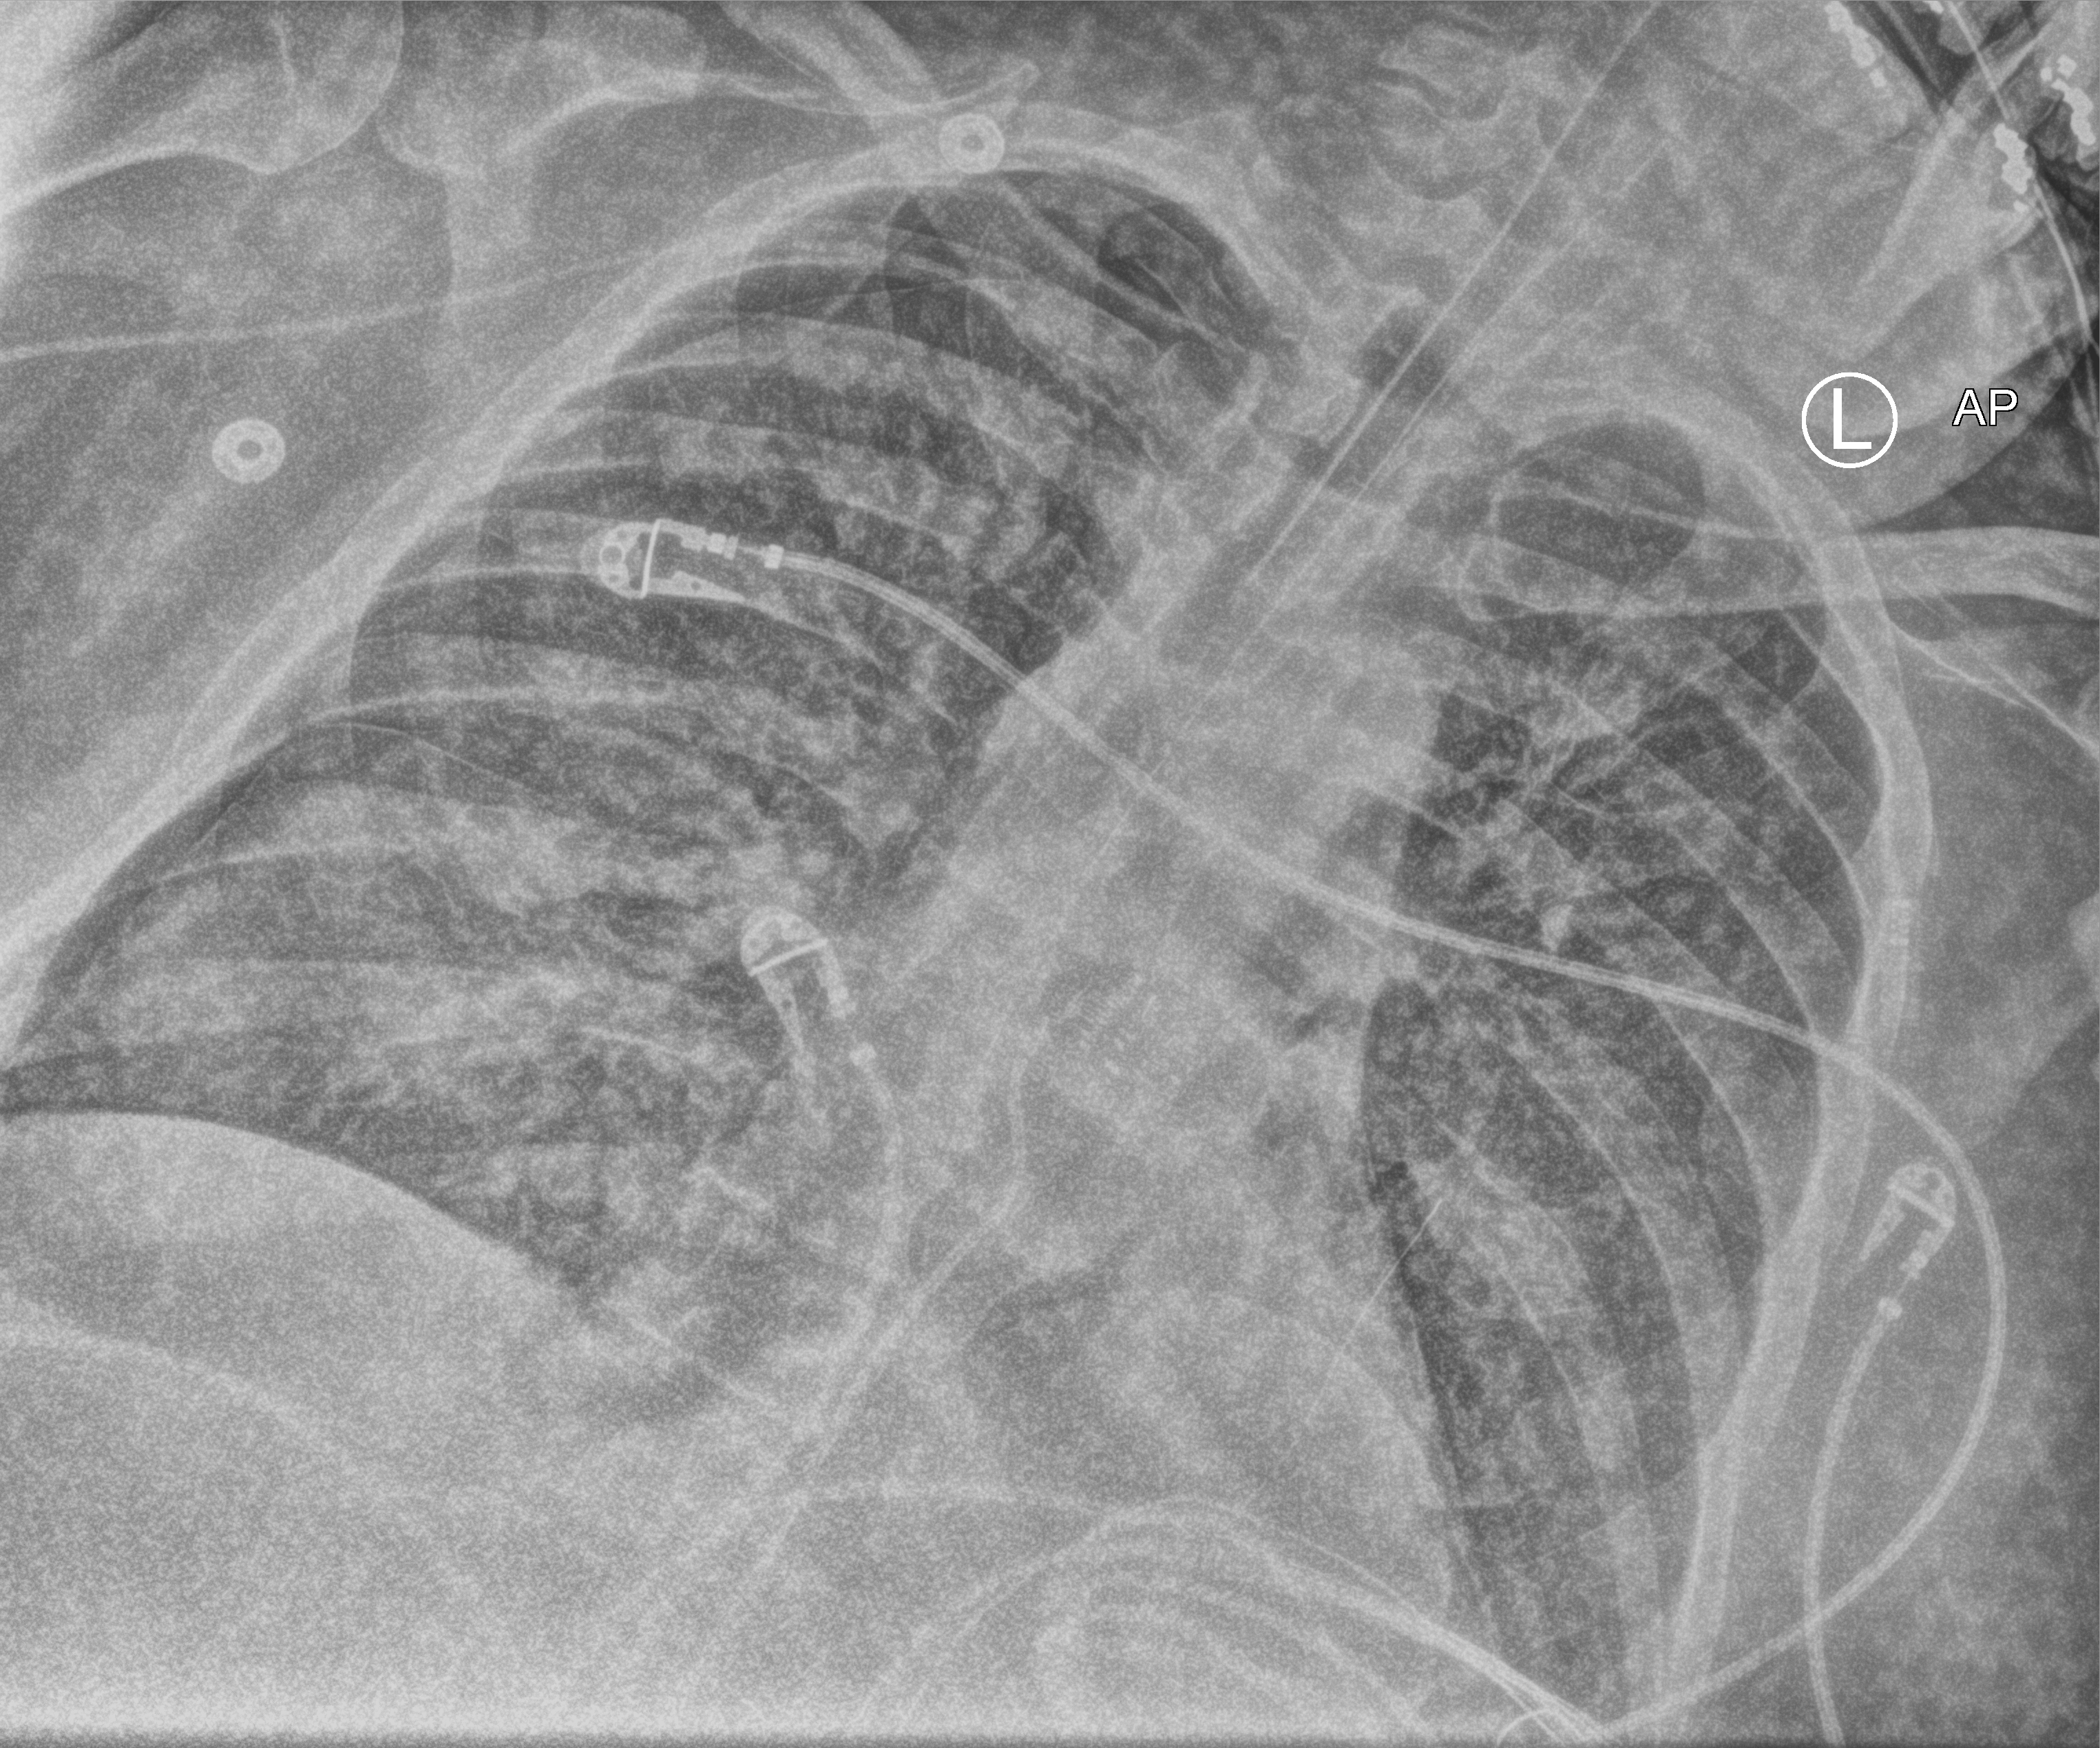
Portable chest radiograph, anteroposterior (AP) projection. Patient hospitalised with COVID-19, aged 18–59 years.
Hospital-stay facts (about this admission, not read from this image; timing relative to this image not recorded):
- smoking status (admission record): never